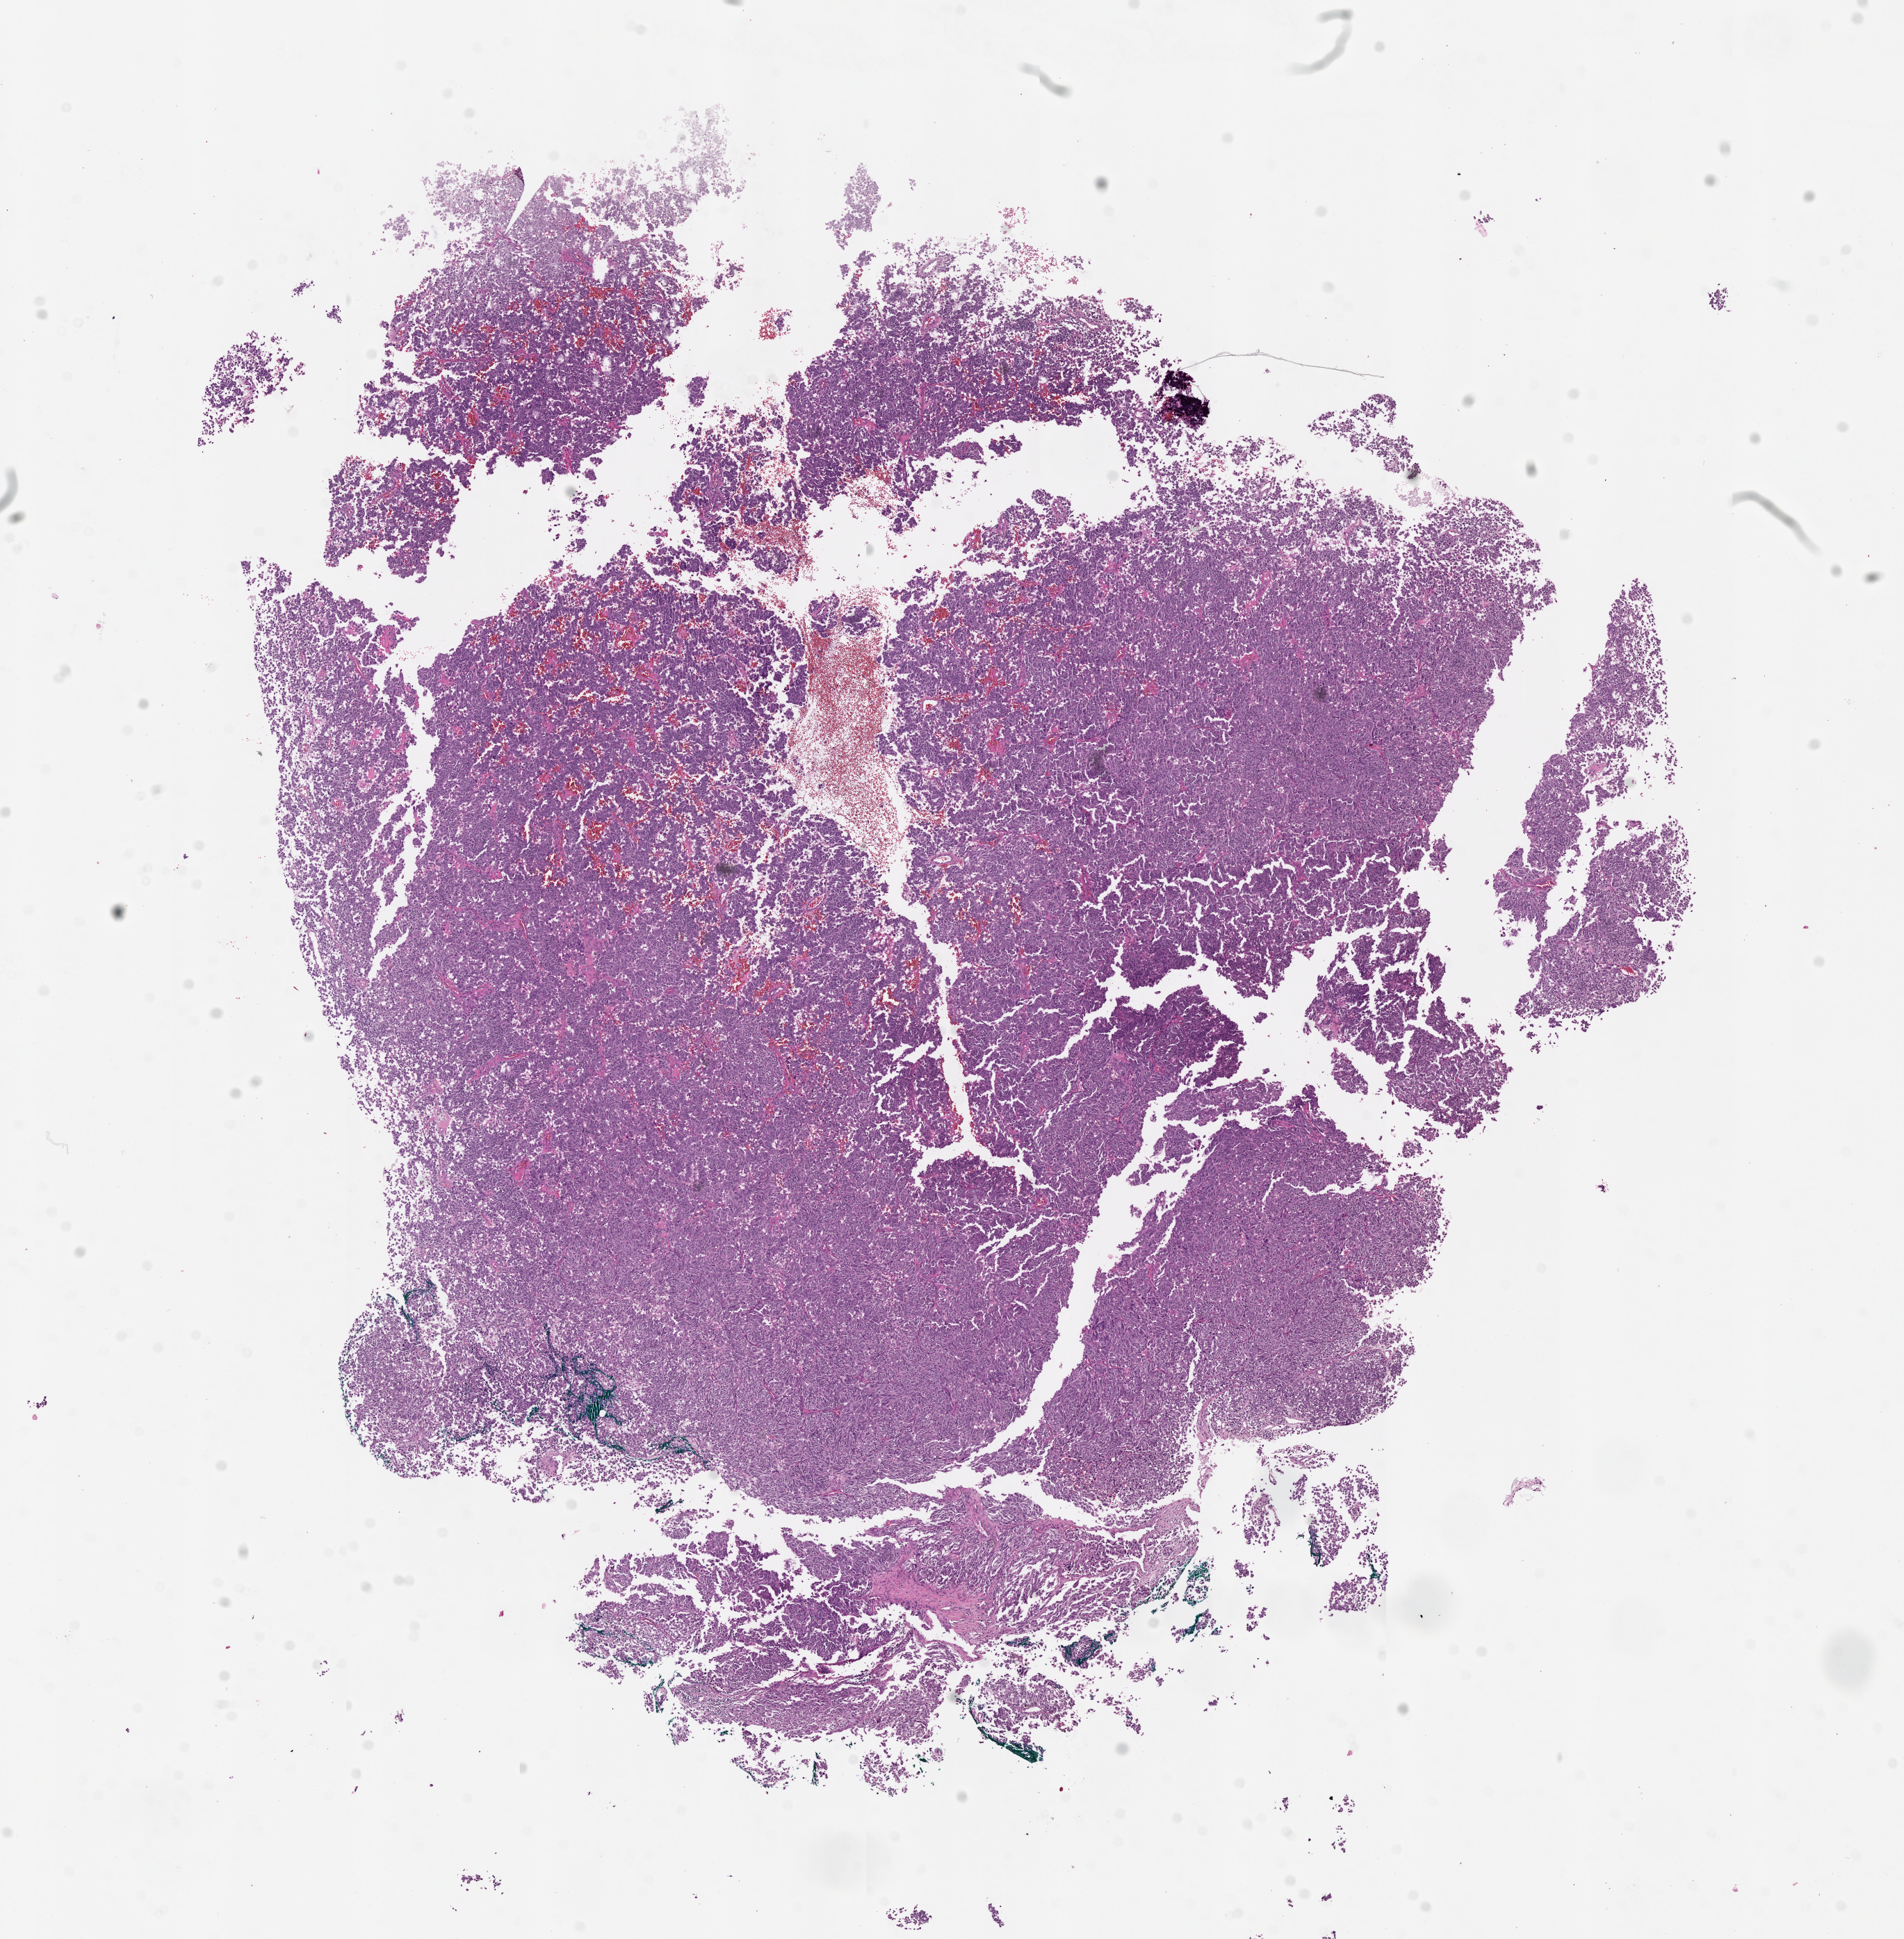
Whole-slide histology image, H&E — whole scanned area (about 11.0 x 11.2 mm) shown as a low-resolution overview. 41-year-old male patient.
- patient diagnosis: Malignant melanoma, NOS